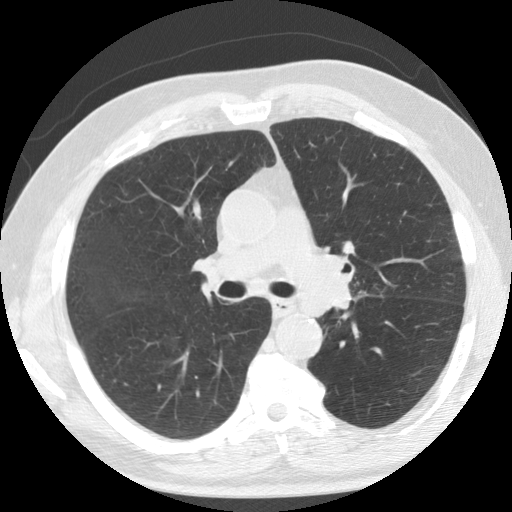
Low-dose screening chest CT, one axial slice. Position 82 of 133 along the scan axis. Reconstruction kernel STANDARD. 120 kVp. Lung window (W 1500 / L -600 HU). 2.5 mm slice thickness. 512 × 512 image matrix.
Outlined on this slice (manually delineated by an expert):
- lesion 1 (tumor, upper lobe of left lung): box from (x=310, y=253) to (x=350, y=316) px